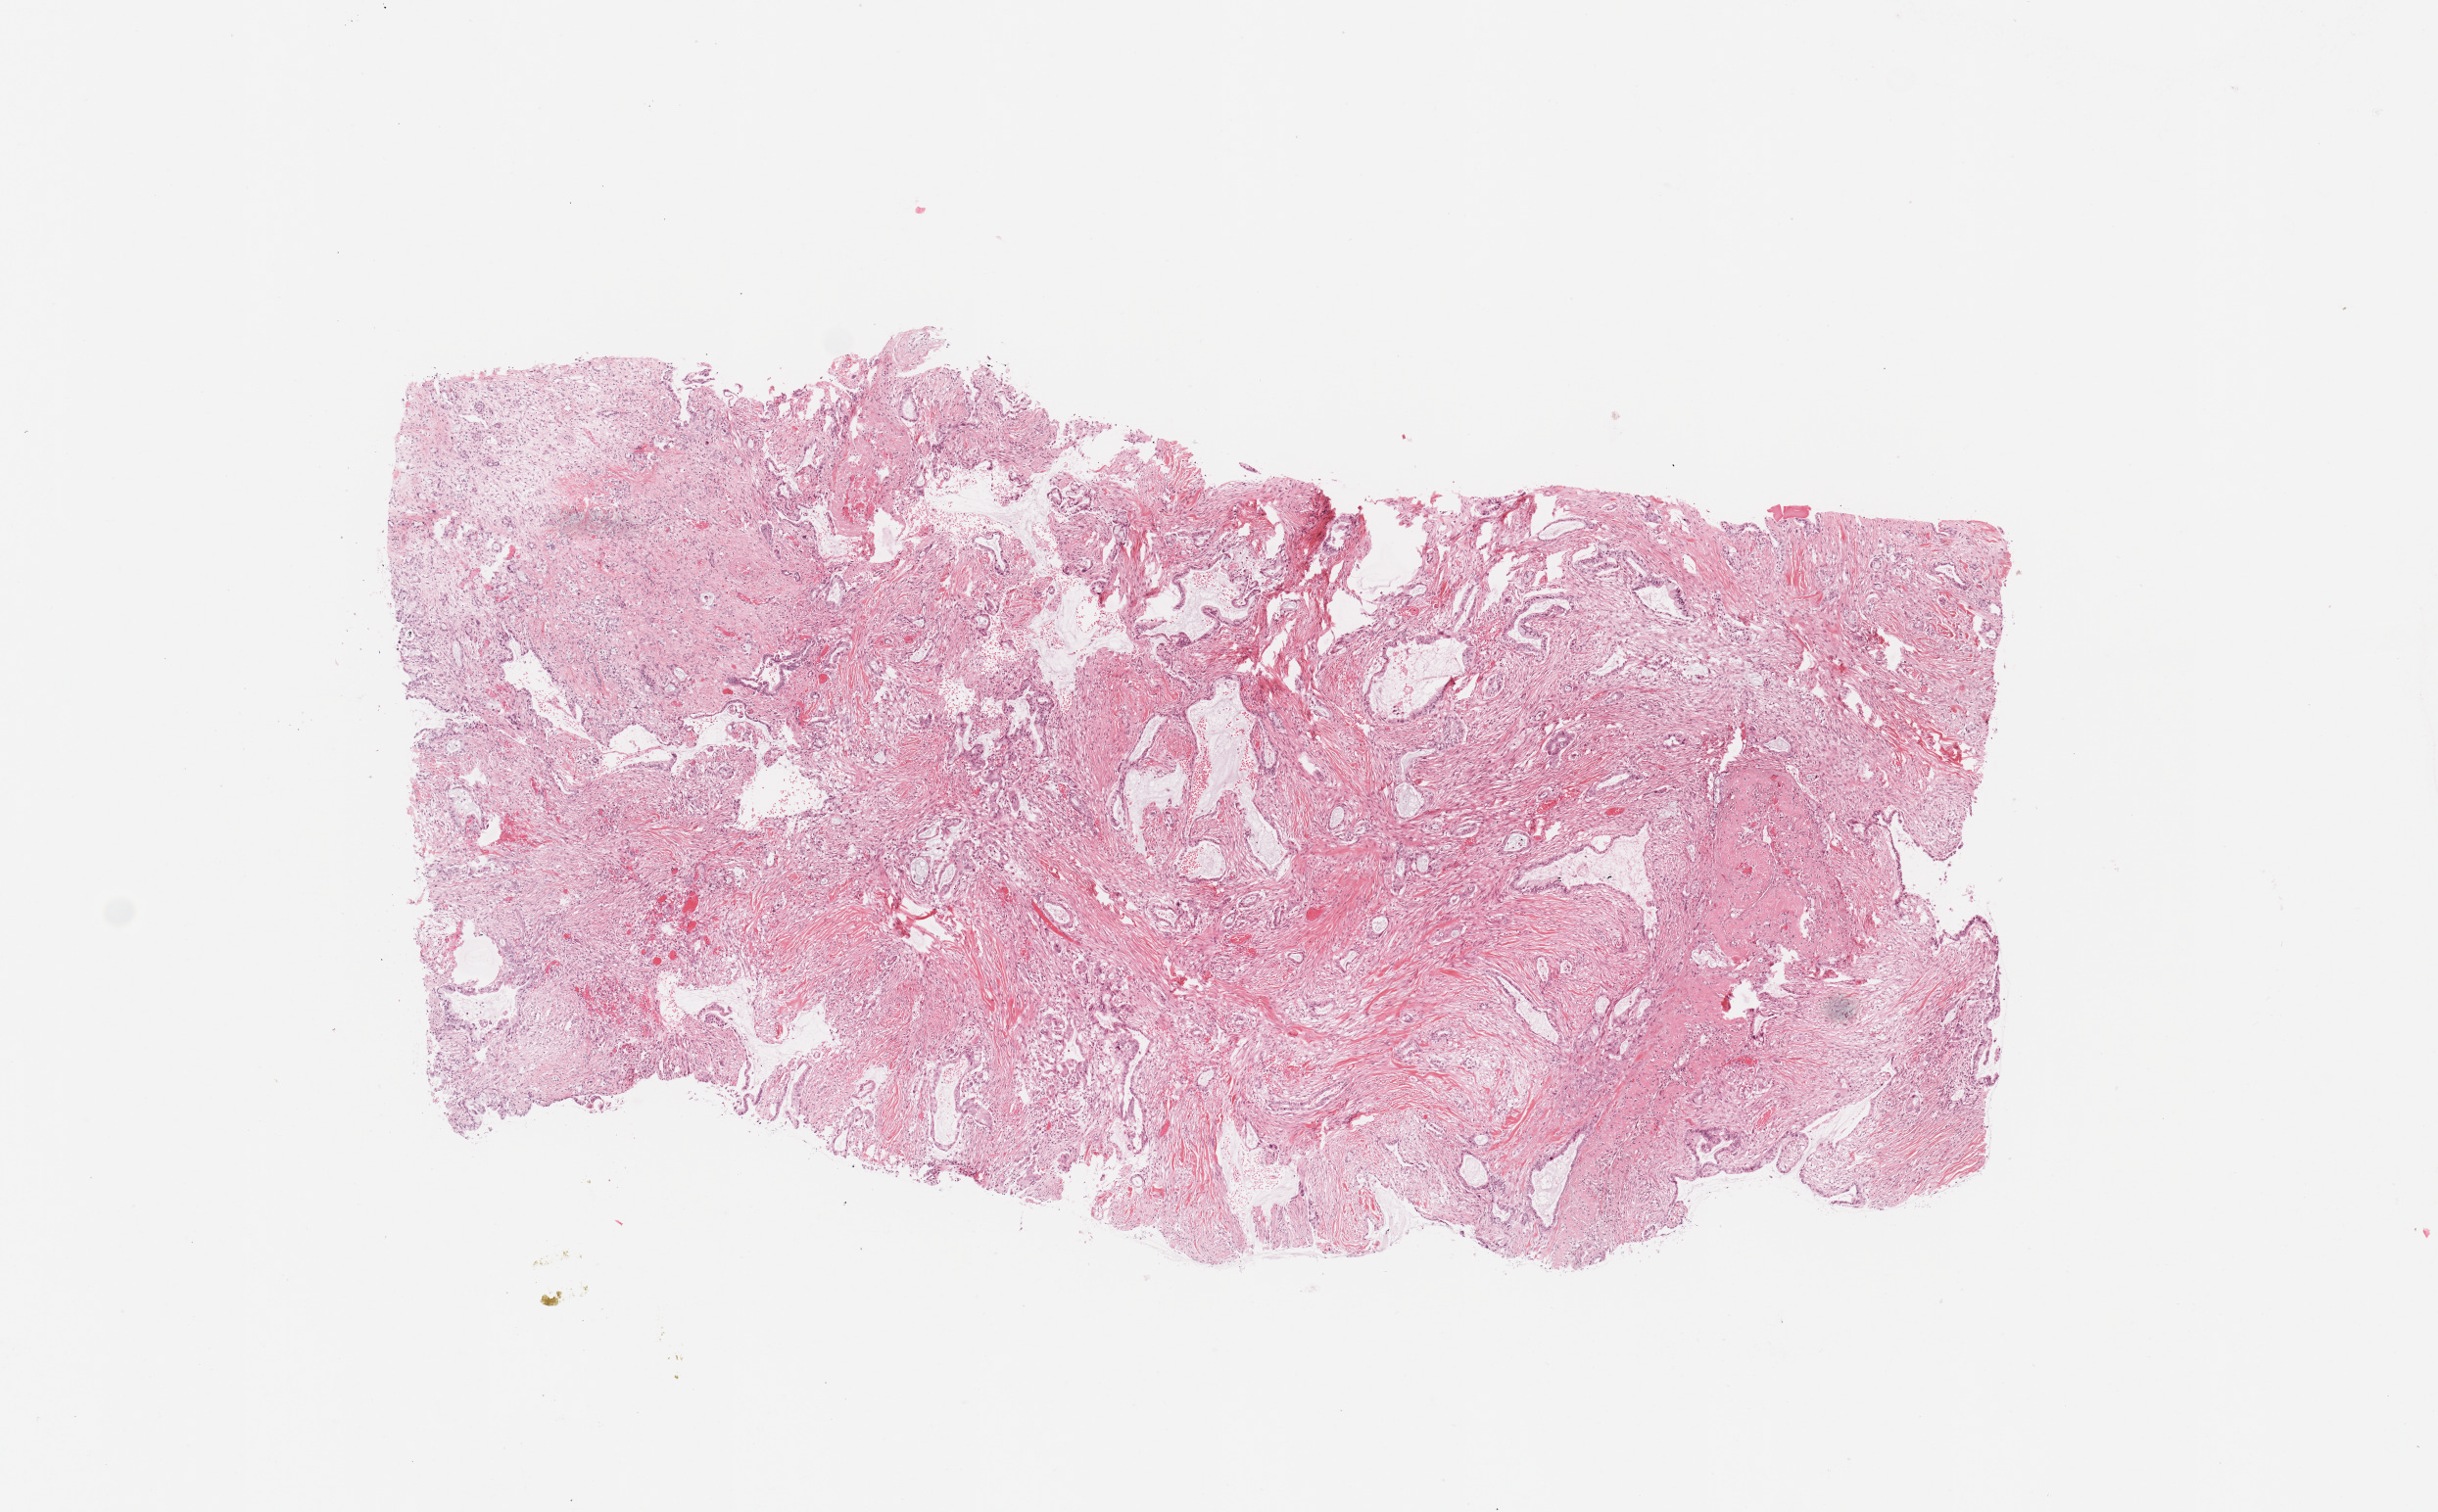
Whole-slide histology image, Hematoxylin and eosin (H&E) stained — whole scanned area (about 9.8 x 6.1 mm, slide scanned at 20x) shown as a low-resolution overview, tumour tissue sample, sampled site: pancreas. Male, 42 y/o. Histologic grade: G3 (poorly differentiated). Composition of this section per pathologist review: tumour nuclei 50%, necrosis 0%.
AJCC pathologic stage: III. Primary tumour site (as recorded): head. Histologic diagnosis: Infiltrating duct carcinoma, NOS.